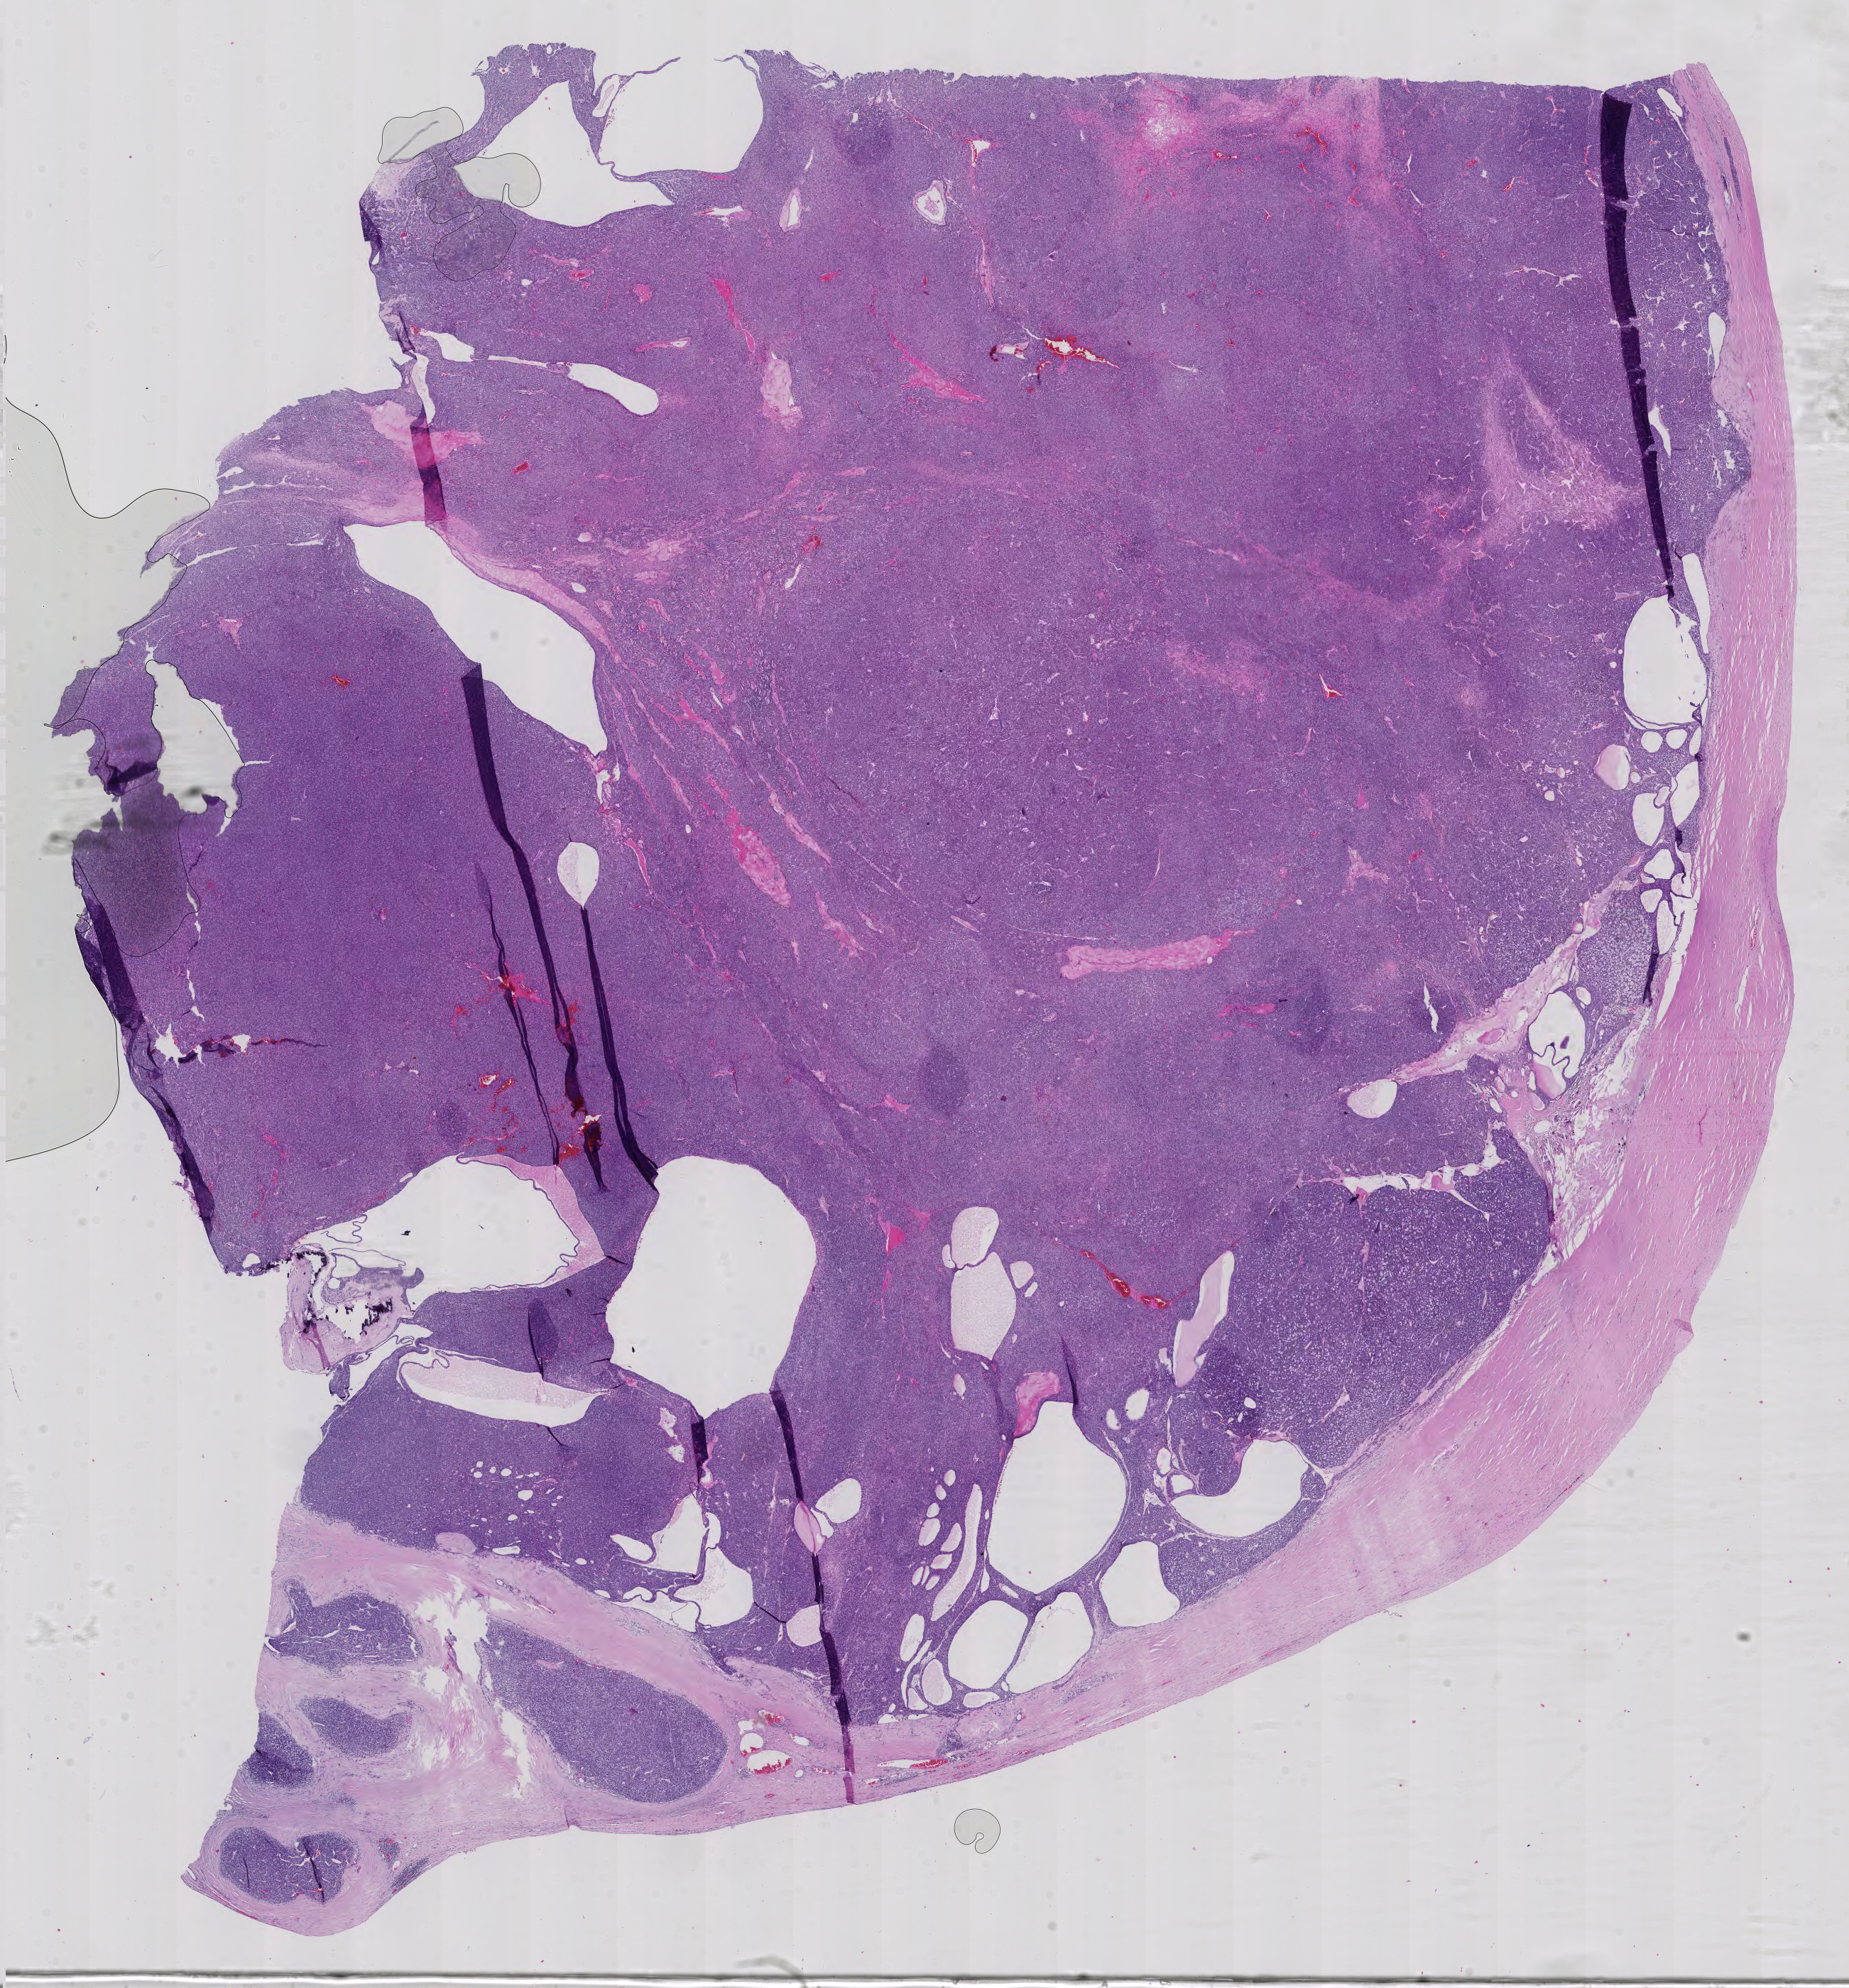
Whole-slide histology image, Hematoxylin and eosin (H&E) stained — whole scanned area (about 19.0 x 20.4 mm, slide scanned at 40x) shown as a low-resolution overview, formalin-fixed paraffin-embedded (FFPE) diagnostic section, primary tumour sample from the thymus. Female, age 75 years at initial diagnosis.
Histologic diagnosis: Thymoma, type A, malignant.